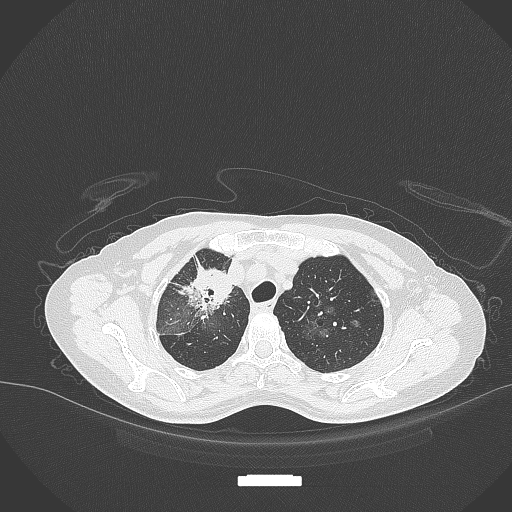
Chest CT, one axial slice; position 262 of 284 along the scan axis; reconstruction kernel B70f; 120 kVp; lung window (W 1500 / L -600 HU); 1 mm slice thickness; 512 × 512 image matrix, field of view 400 × 400 mm. Patient: female, 59 years. From the clinical record (not read from this slice): clinical TNM (as recorded): T3 N0 M0; histopathological grade: G1.
Annotated regions visible in this slice (rectangle marked by the reading radiologist):
- lung tumour (recorded histology: adenocarcinoma): bounding box [x1, y1, x2, y2] px = [180, 262, 233, 313]